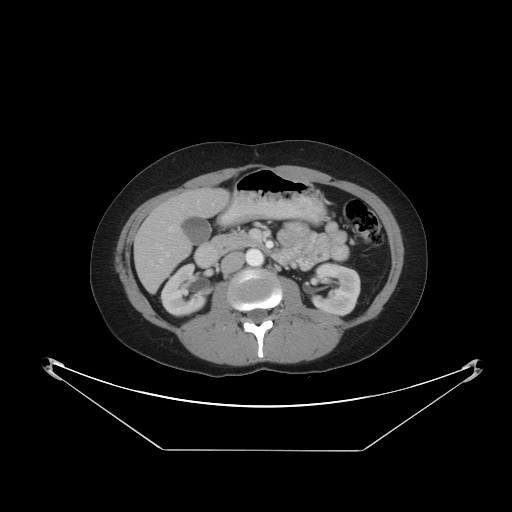
Contrast-enhanced abdominal CT, one axial slice. Position 18 of 48 along the scan axis. Reconstruction kernel STANDARD. Intravenous contrast given. Soft-tissue window (W 400 / L 40 HU). 512 × 512 image matrix, field of view 482 × 482 mm. Female patient, age 38 years. From the clinical record (not read from this slice): diagnosis: colorectal cancer liver metastases, imaged before liver resection; multiple liver metastases: yes; largest metastasis: 2.5 cm; chemotherapy before resection: no.
Structures marked on this image (expert manual segmentation):
- hepatic veins: box from (x=169, y=226) to (x=174, y=231) px
- liver: (x=135, y=188)–(x=229, y=290)
- planned liver remnant (the part of the liver to remain after resection): (x=172, y=188)–(x=229, y=218)
- portal vein (with intrahepatic branches): (x=160, y=204)–(x=213, y=262)